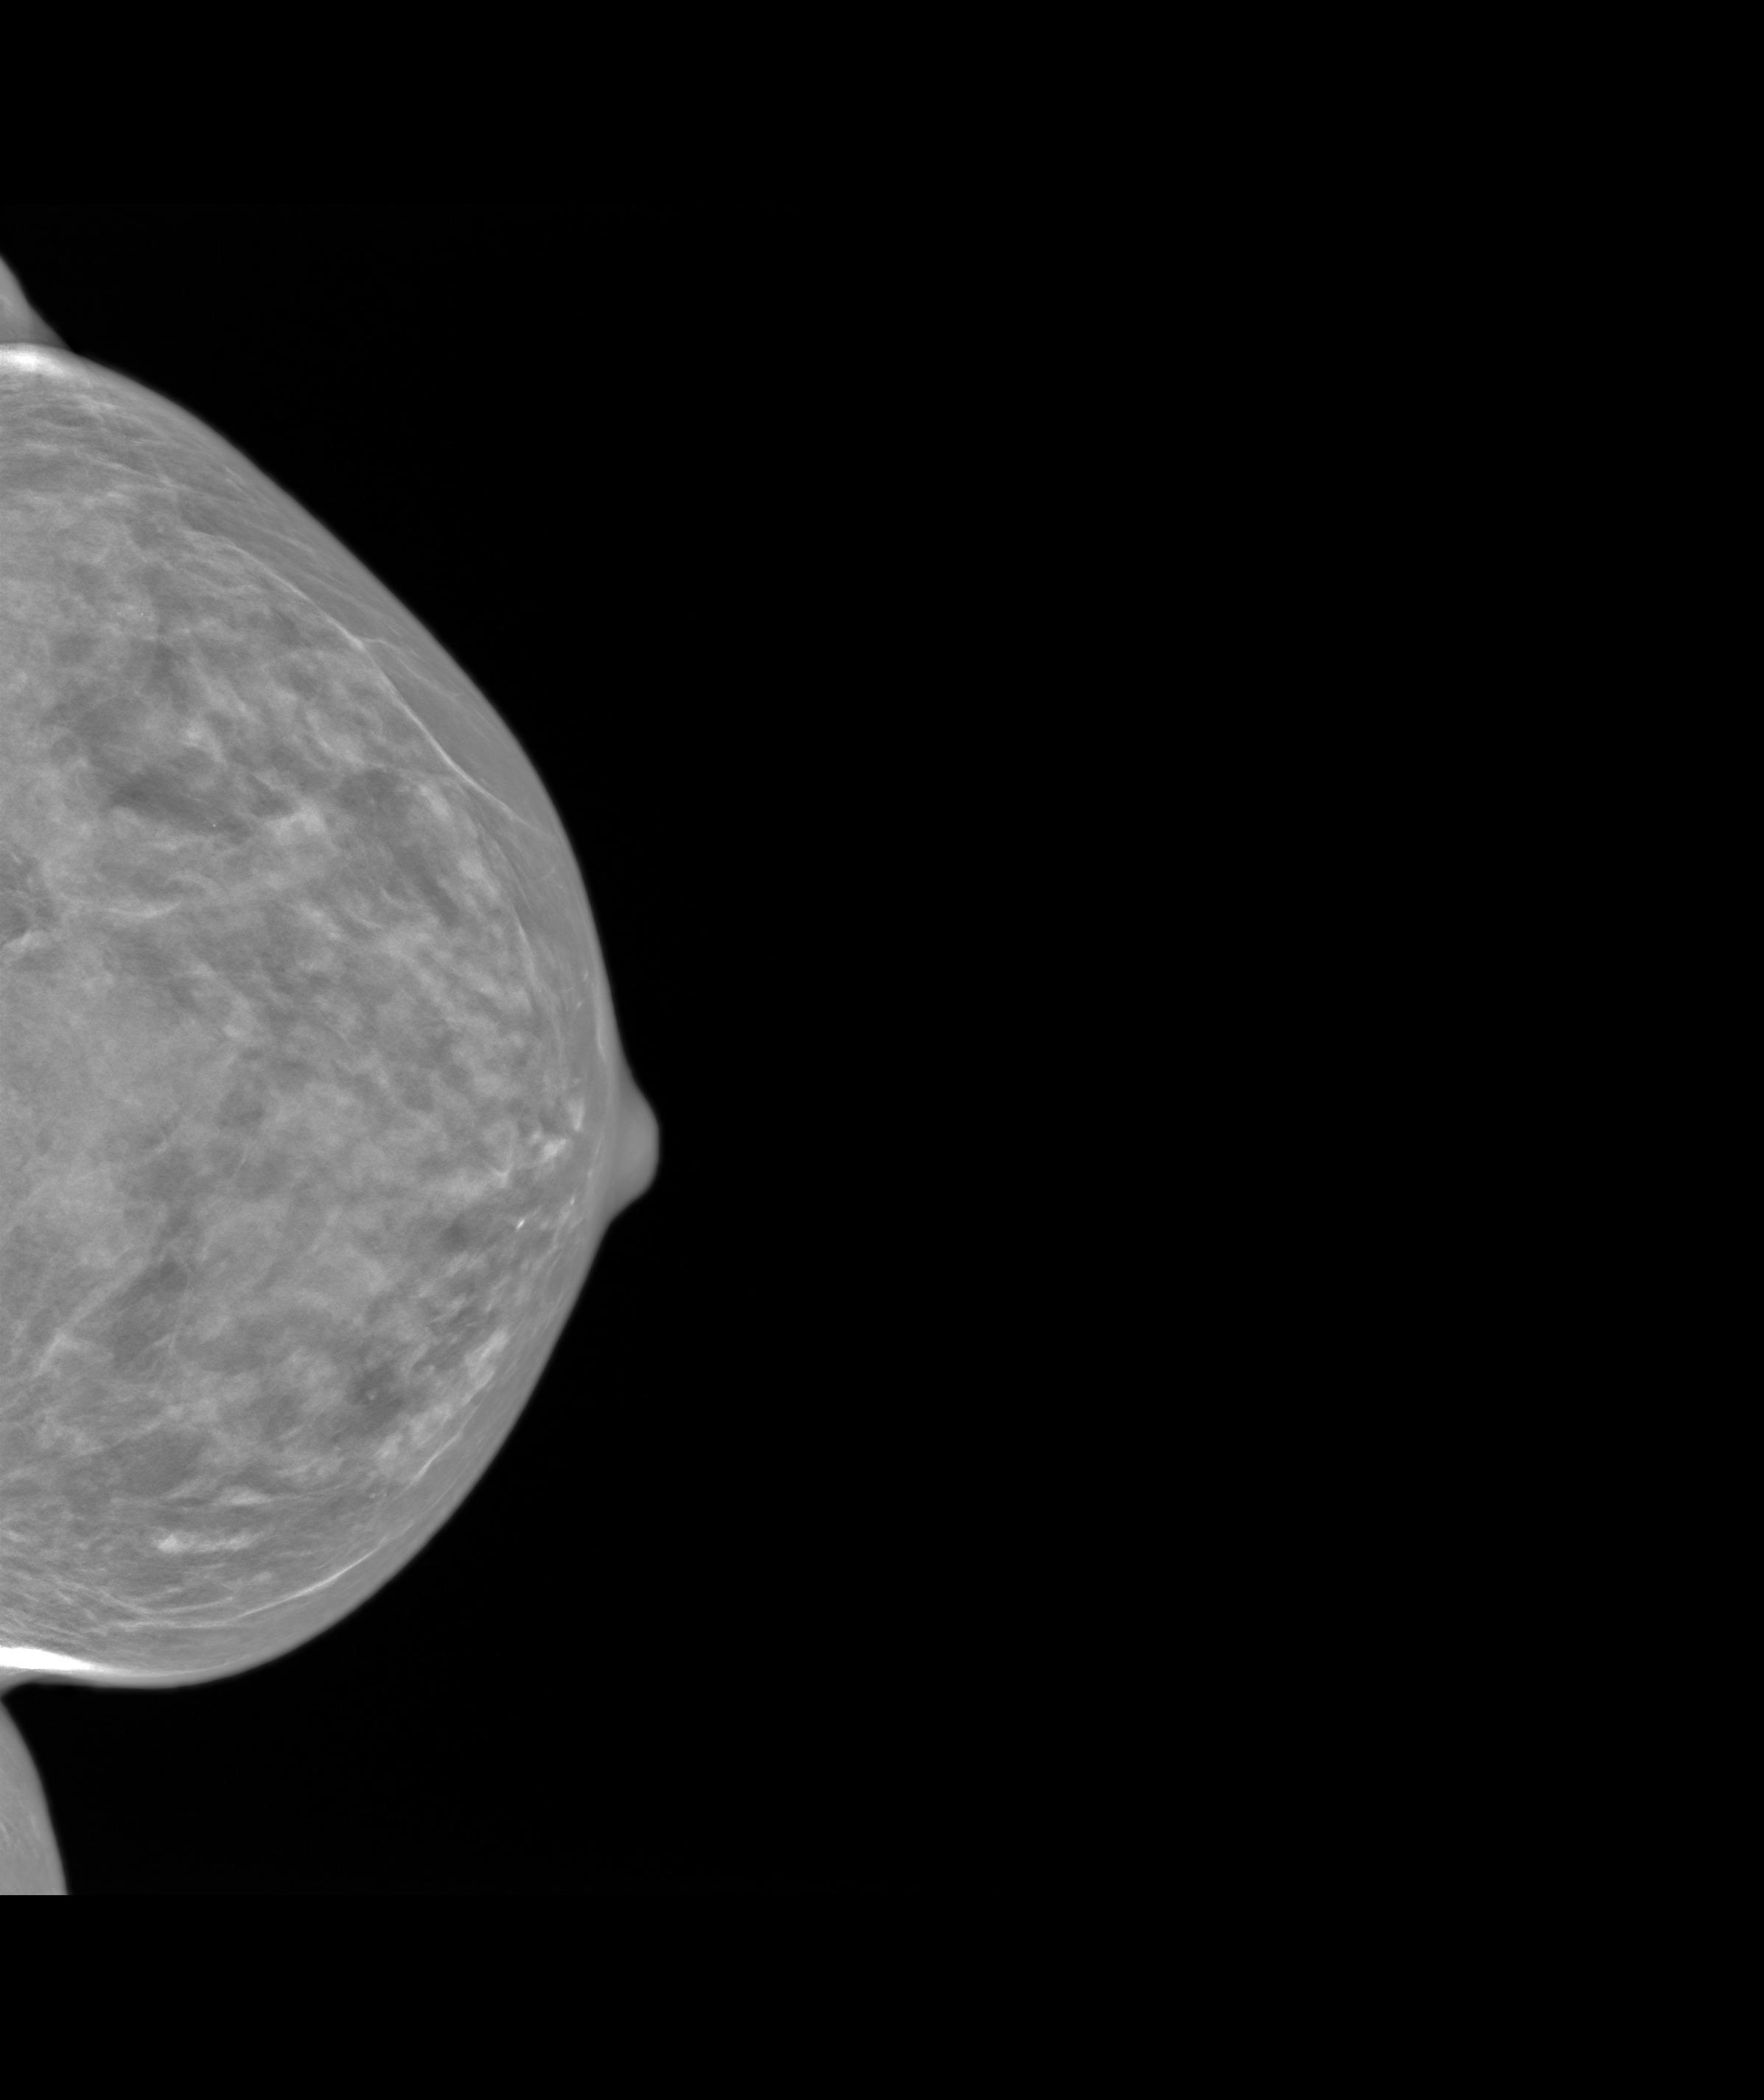
Screening examination. Patient: female, 74 years.
Image type: synthesized 2-D view from tomosynthesis. Breast: left. Projection: CC view.